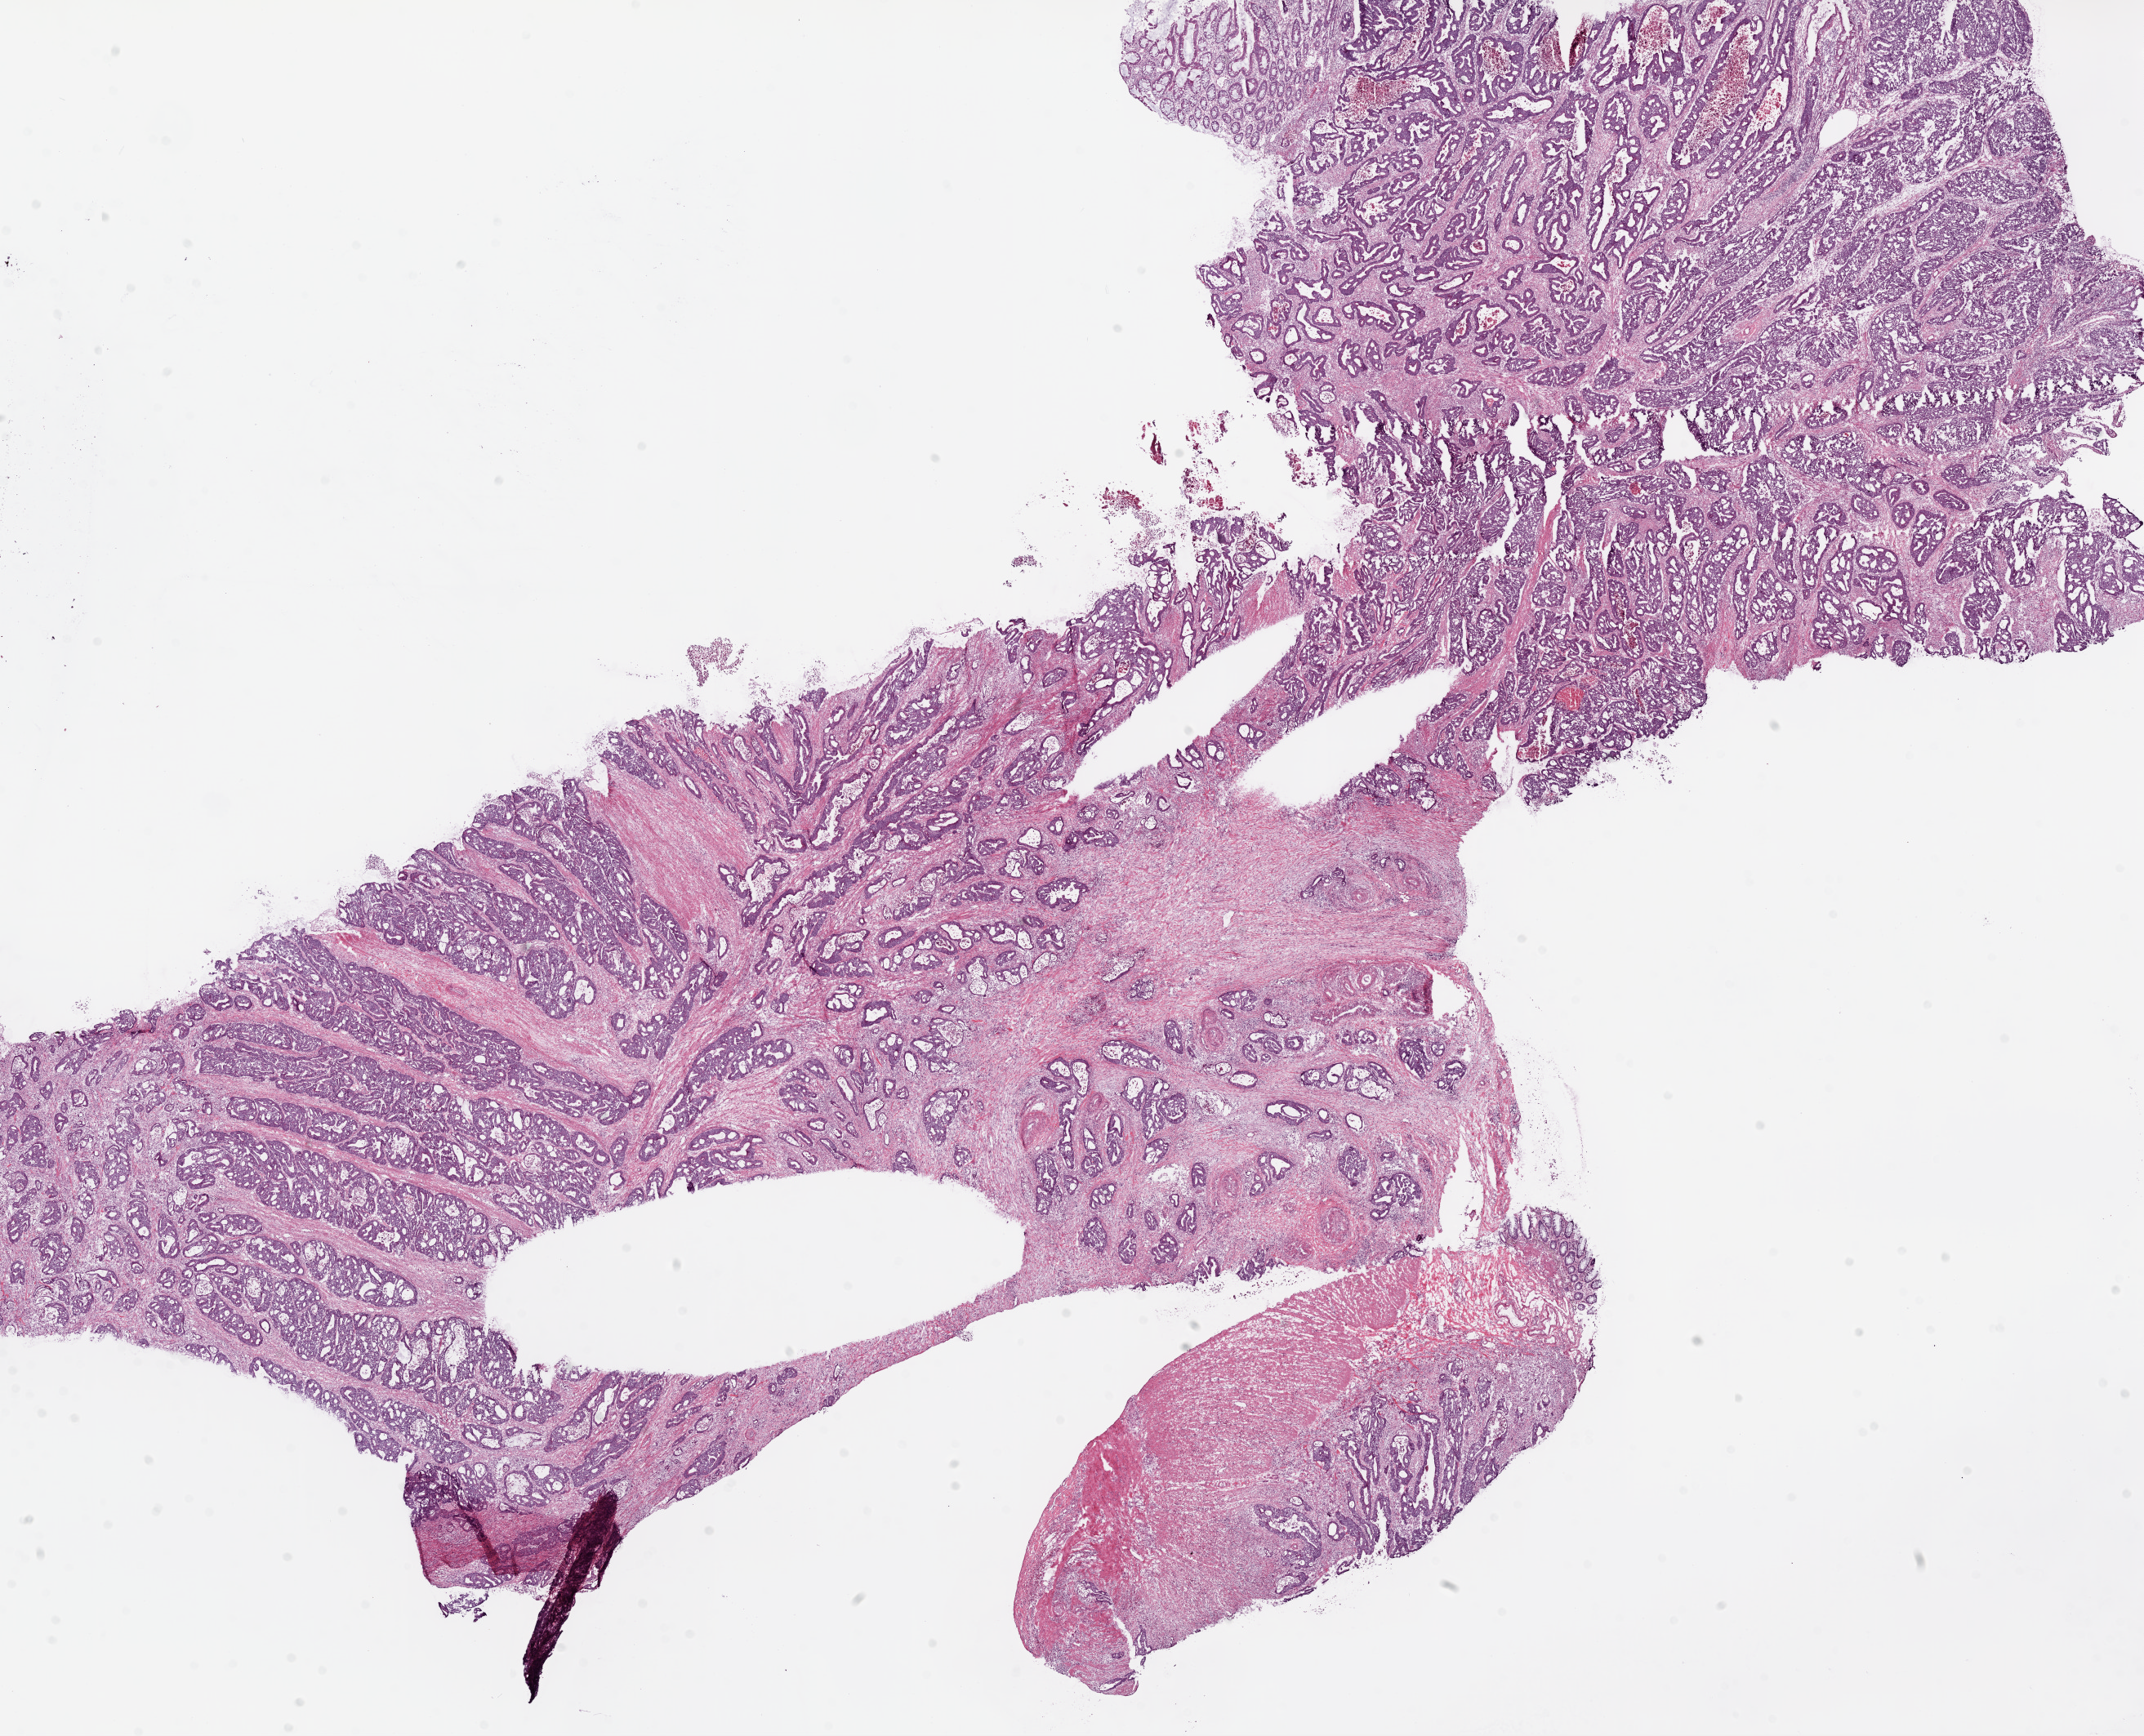
H&E whole-slide image — low-resolution overview of the scanned area, about 21.1 x 17.1 mm (acquisition: 20x scan), frozen section from the bottom of the tissue portion, sample: primary tumour, colon. Female patient; age at initial diagnosis 39 years. Composition of this section per pathologist review: tumour cells 98%, tumour nuclei 85%, normal cells 0%, stromal cells 0%, necrosis 2%. Infiltration values recorded for this section: lymphocyte infiltration 5%, monocyte infiltration 1%, neutrophil infiltration 1%.
Histologic diagnosis: Adenocarcinoma, NOS (sigmoid colon). AJCC pathologic stage: IIIB (7th edition). Lymph nodes positive (case pathology): 3 of 108 examined. TNM: T3 N1b M0.